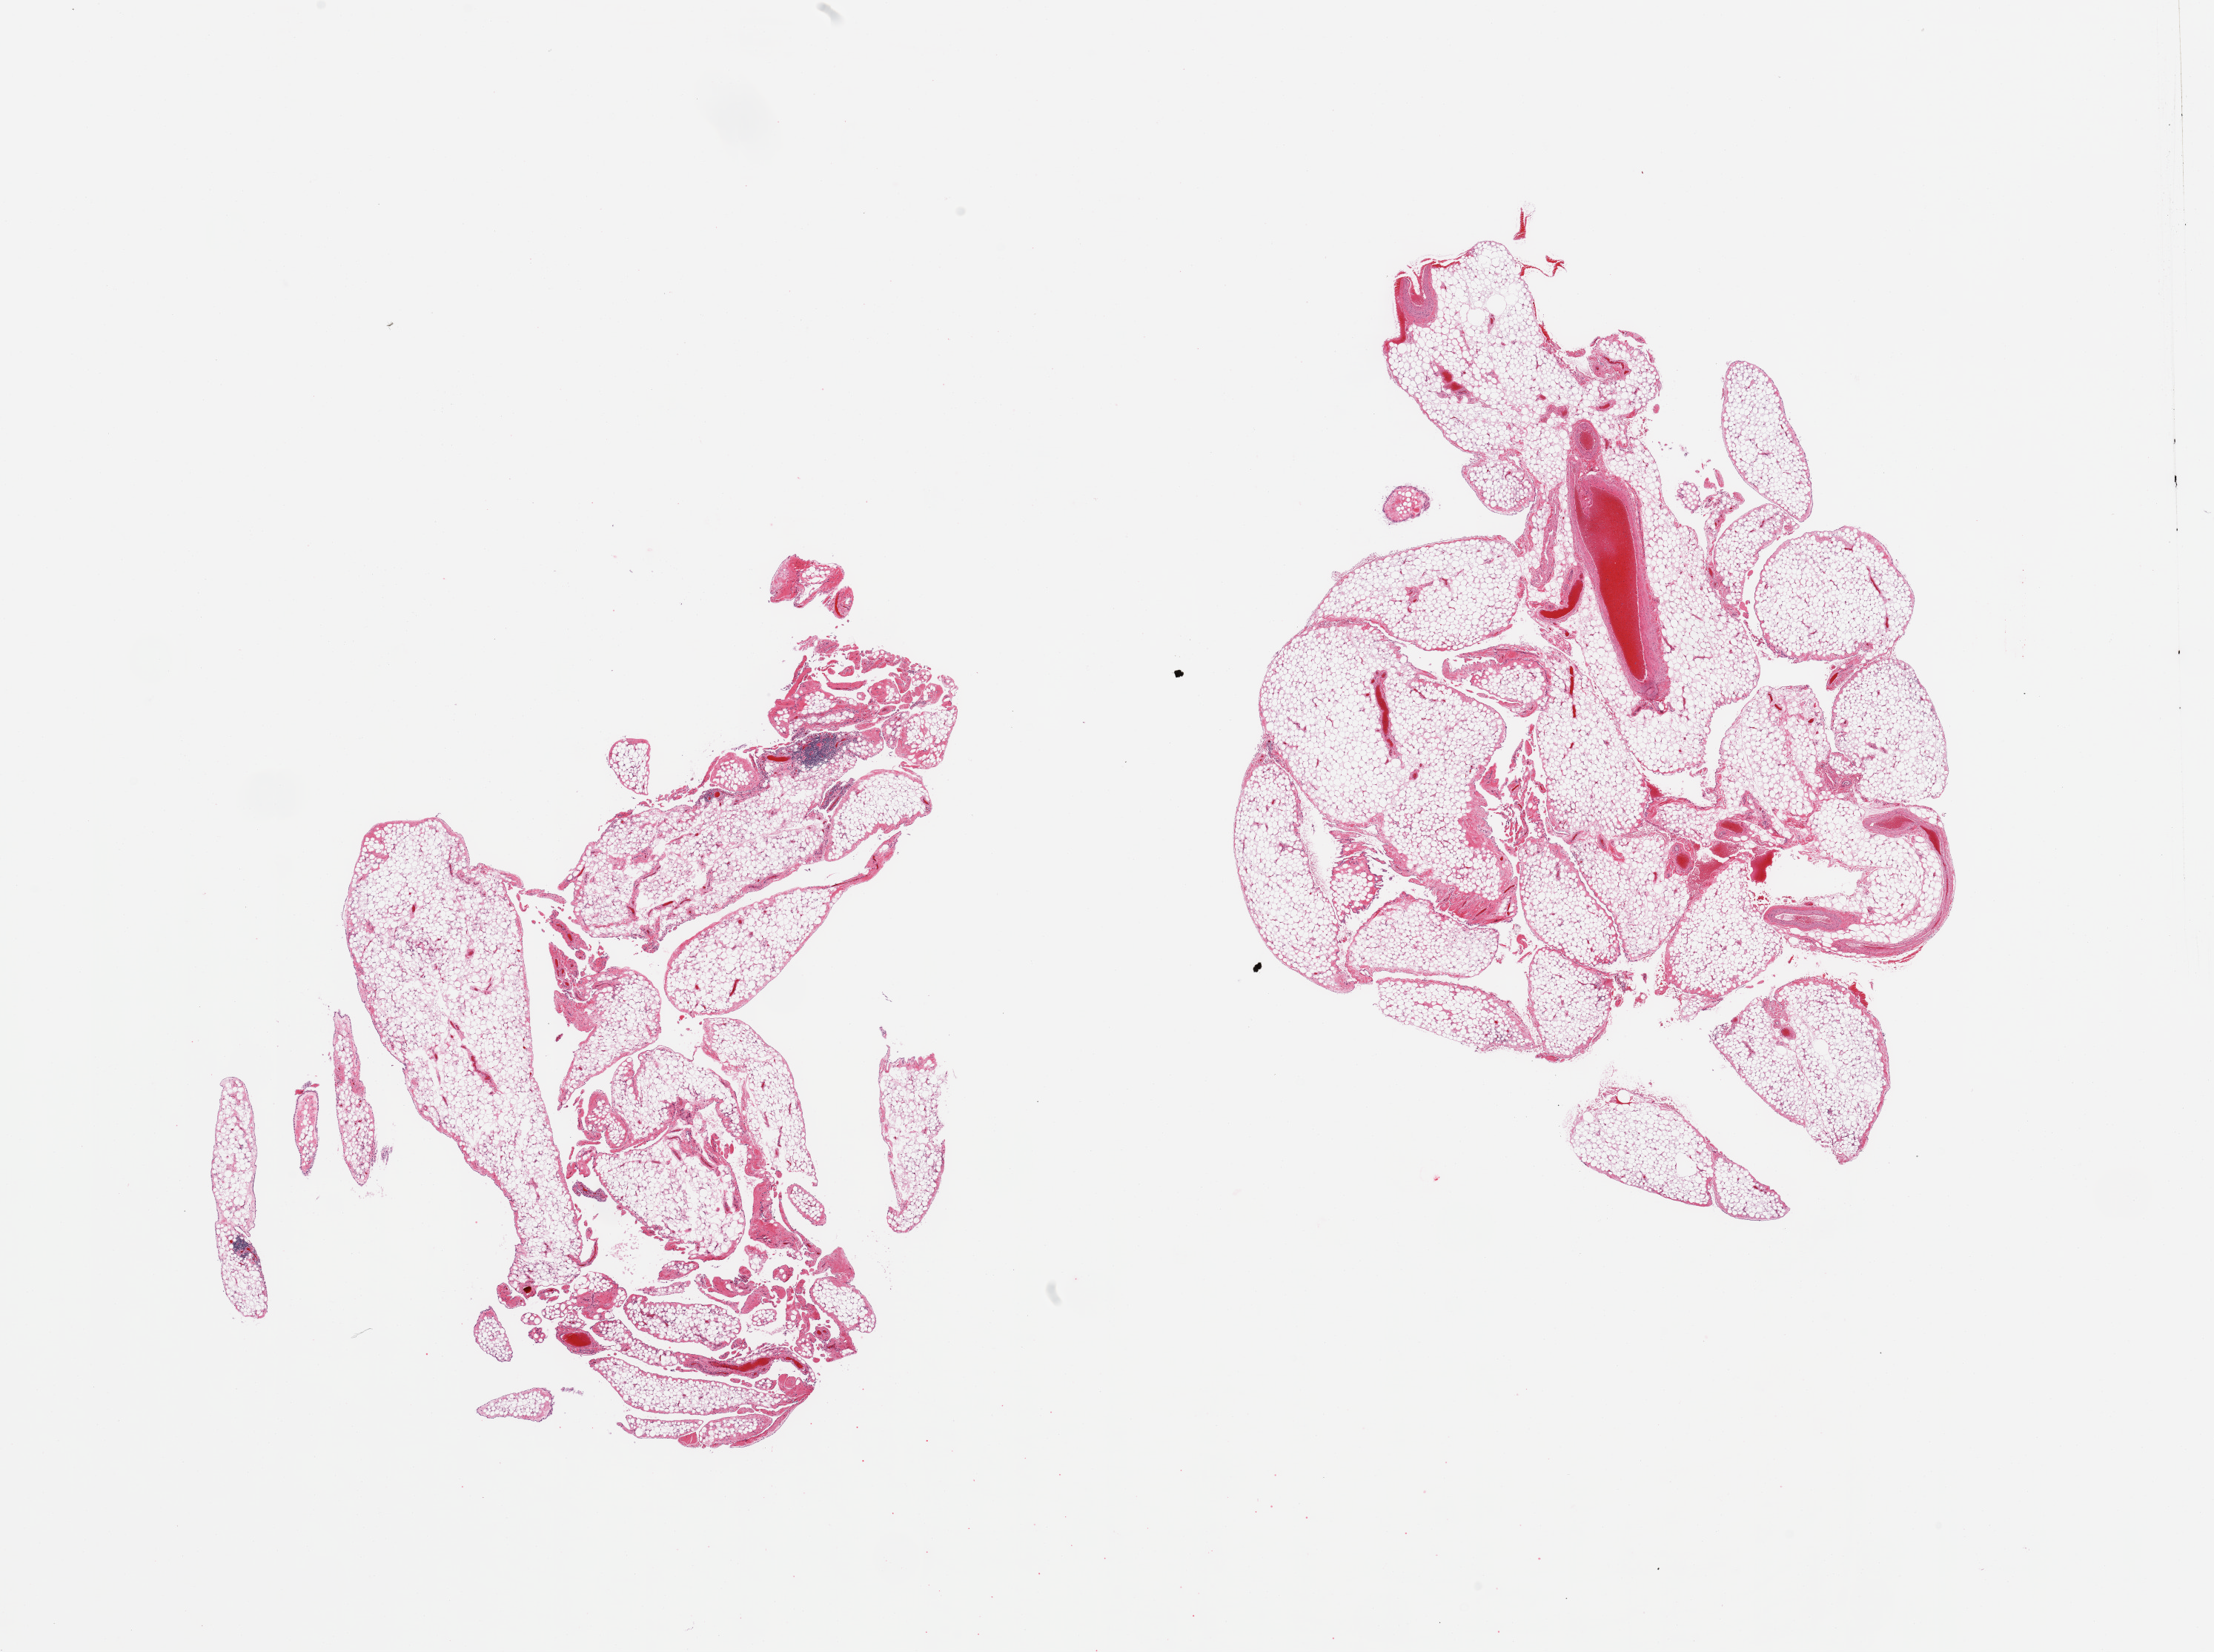
Whole-slide image, haematoxylin and eosin stain, brightfield, shown as a low-resolution overview of the whole scanned area (about 23.6 x 17.6 mm). PAXgene-fixed paraffin-embedded (PFPE) section. Sampled site (target tissue): omentum. Donor tissue sample.
Pathologist's review note for this sample: 2 pieces; 5% fibrovascular content.